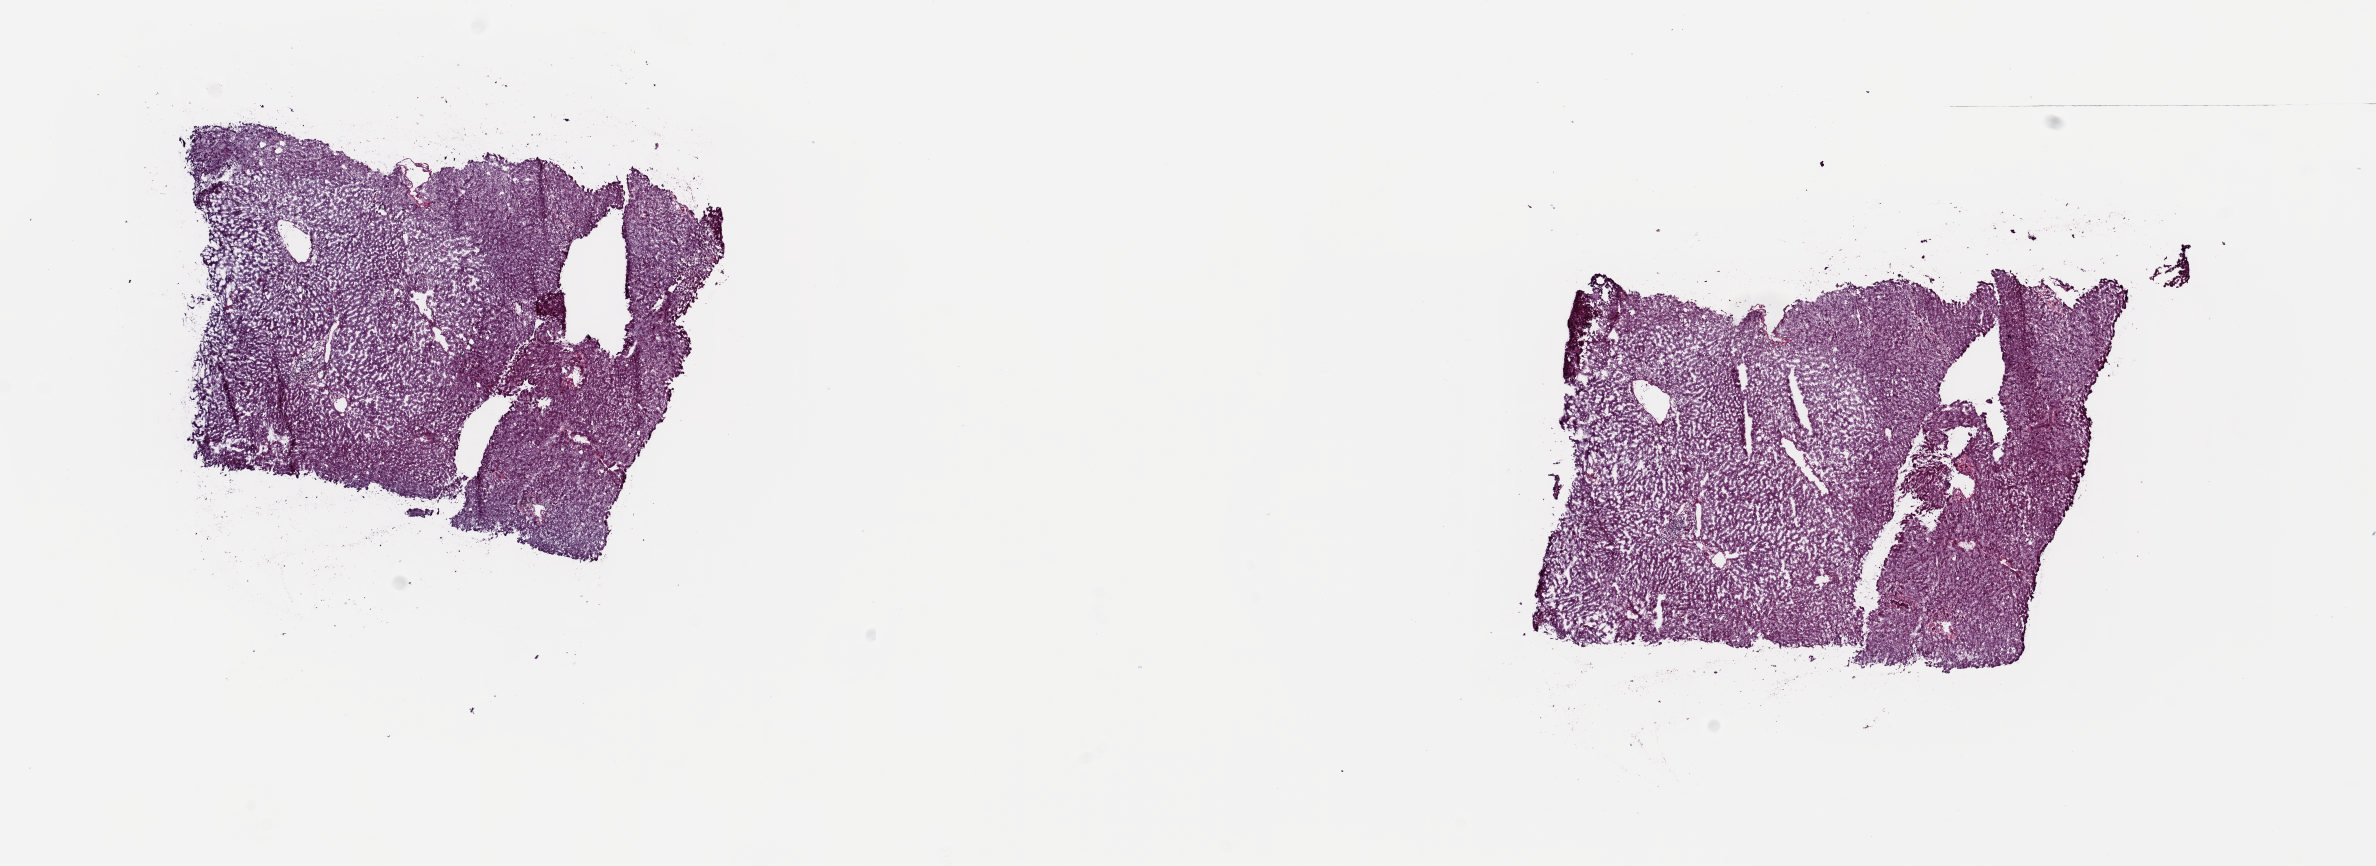
Whole-slide histology image, Hematoxylin and eosin (H&E) stained — a low-resolution overview of the entire scanned area, about 18.8 x 6.9 mm (acquisition: 20x scan). Frozen section from the top of the tissue portion. Liver, solid tissue normal (non-tumour tissue) sample. Female patient; age at initial diagnosis 75 years. Slide review estimates, as recorded: tumour cells 0%, tumour nuclei 0%, normal cells 100%, stromal cells 0%, necrosis 0%. Infiltration values recorded for this section: lymphocyte infiltration 0%, monocyte infiltration 0%, neutrophil infiltration 0%.
This section: solid tissue normal sample (biorepository sample class). Patient diagnosis: Hepatocellular carcinoma, NOS.